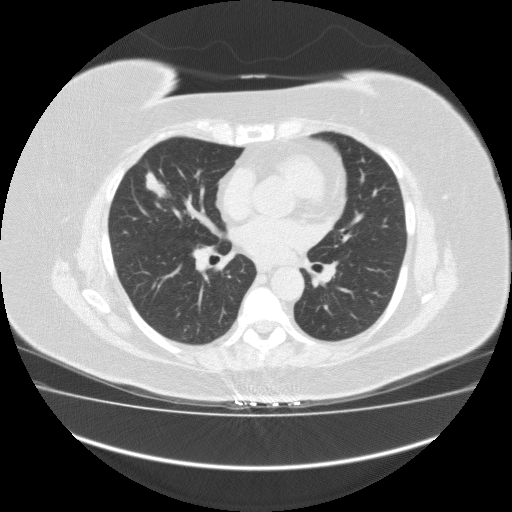
Low-dose screening chest CT, one axial slice; position 85 of 162 along the scan axis; reconstruction kernel FC10; lung window (W 1500 / L -600 HU); 512 × 512 image matrix, field of view 420 × 420 mm.
Structures marked on this image (outlined manually by an expert reader):
- lesion 1 (tumor, middle lobe of right lung): bounding box (x1, y1, x2, y2) in pixels: (146, 172, 171, 199)